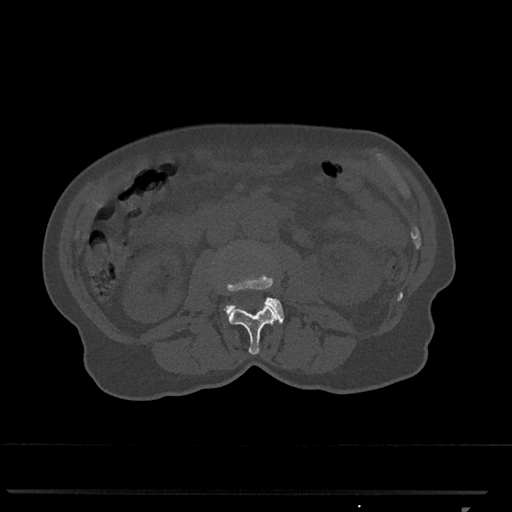
CT including the spine, one axial slice; slice 307 of 793 in the series (ordered by position); 120 kVp; bone window (W 1800 / L 400 HU); 0.5 mm slice thickness; 512 × 512 image matrix, field of view 380 × 380 mm. Female patient, age 62 years. From the clinical record (not read from this slice): primary cancer: renal.
Structures marked on this image (semi-automatically segmented with operator editing):
- L2 vertebra: bounding box [x1, y1, x2, y2] px = [228, 304, 278, 355]
- L3 vertebra: [225, 276, 284, 323]